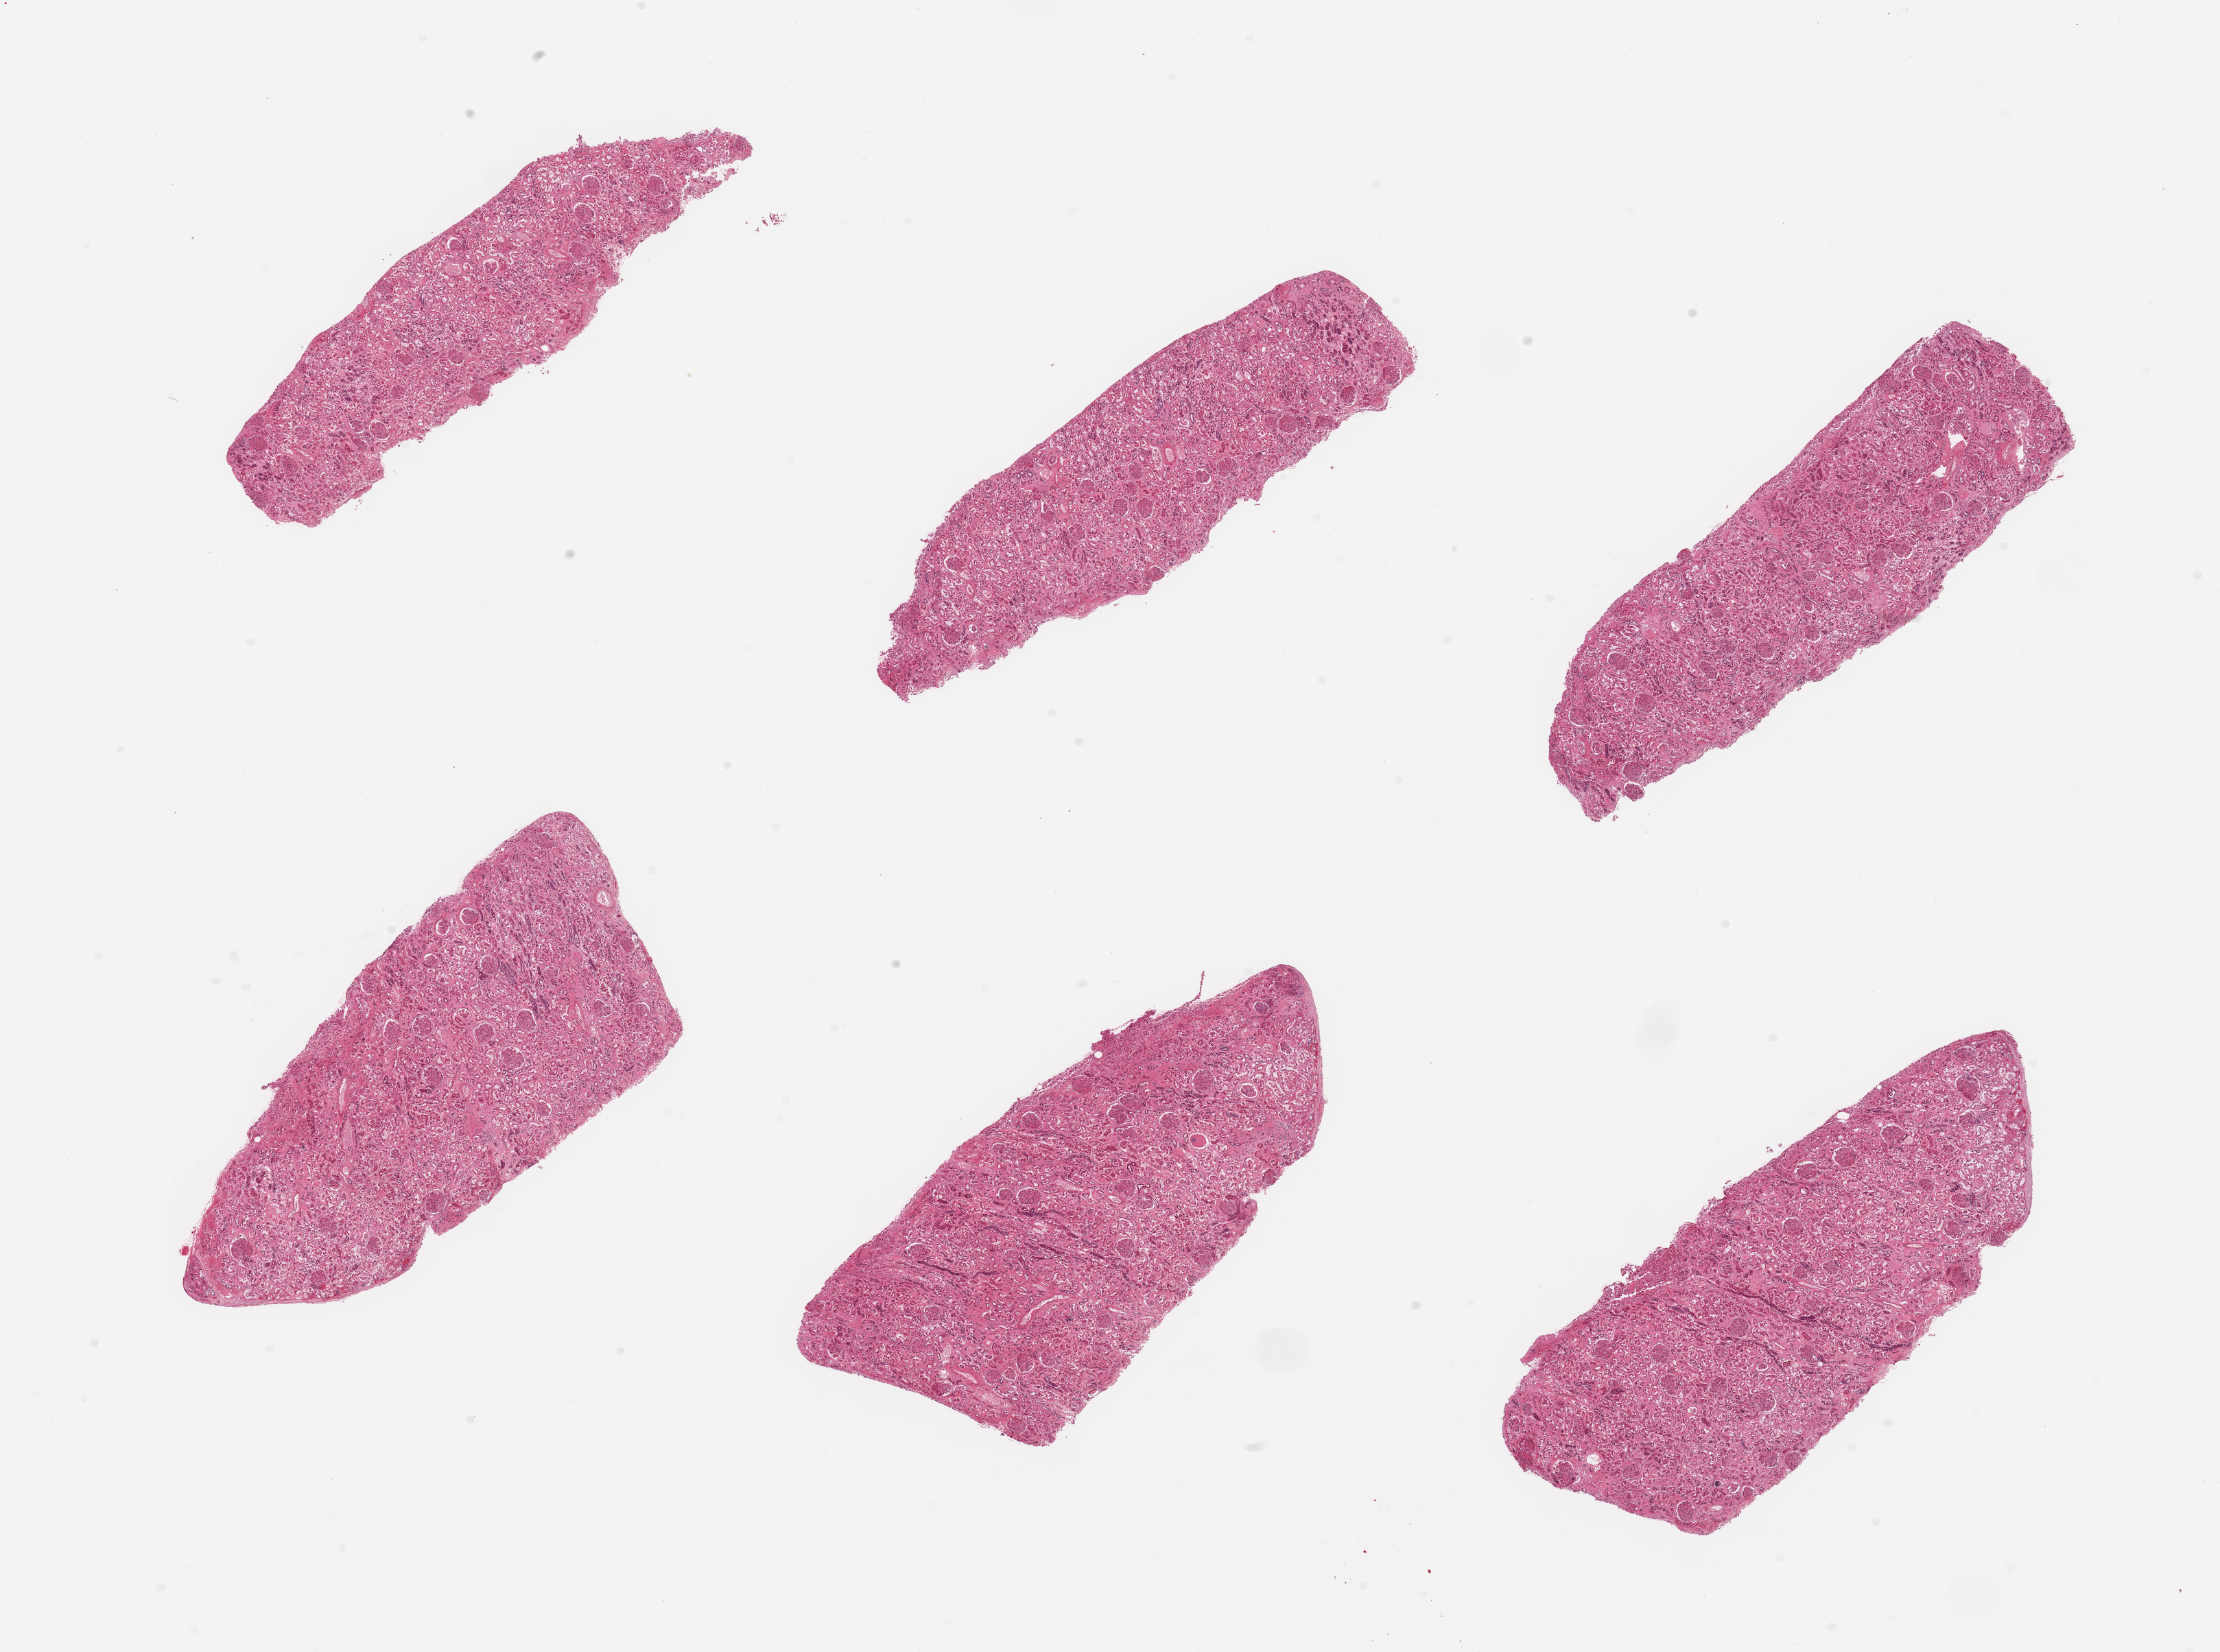
Whole-slide image, H&E stain — shown as a low-resolution overview of the whole scanned area (about 25.6 x 19.0 mm). PAXgene-fixed, paraffin-embedded tissue. Sampled site (target tissue): renal cortex. Donor tissue sample.
Pathologist's review note for this sample: 6 pieces, glomeruli present, tubules moderately autolyzed.